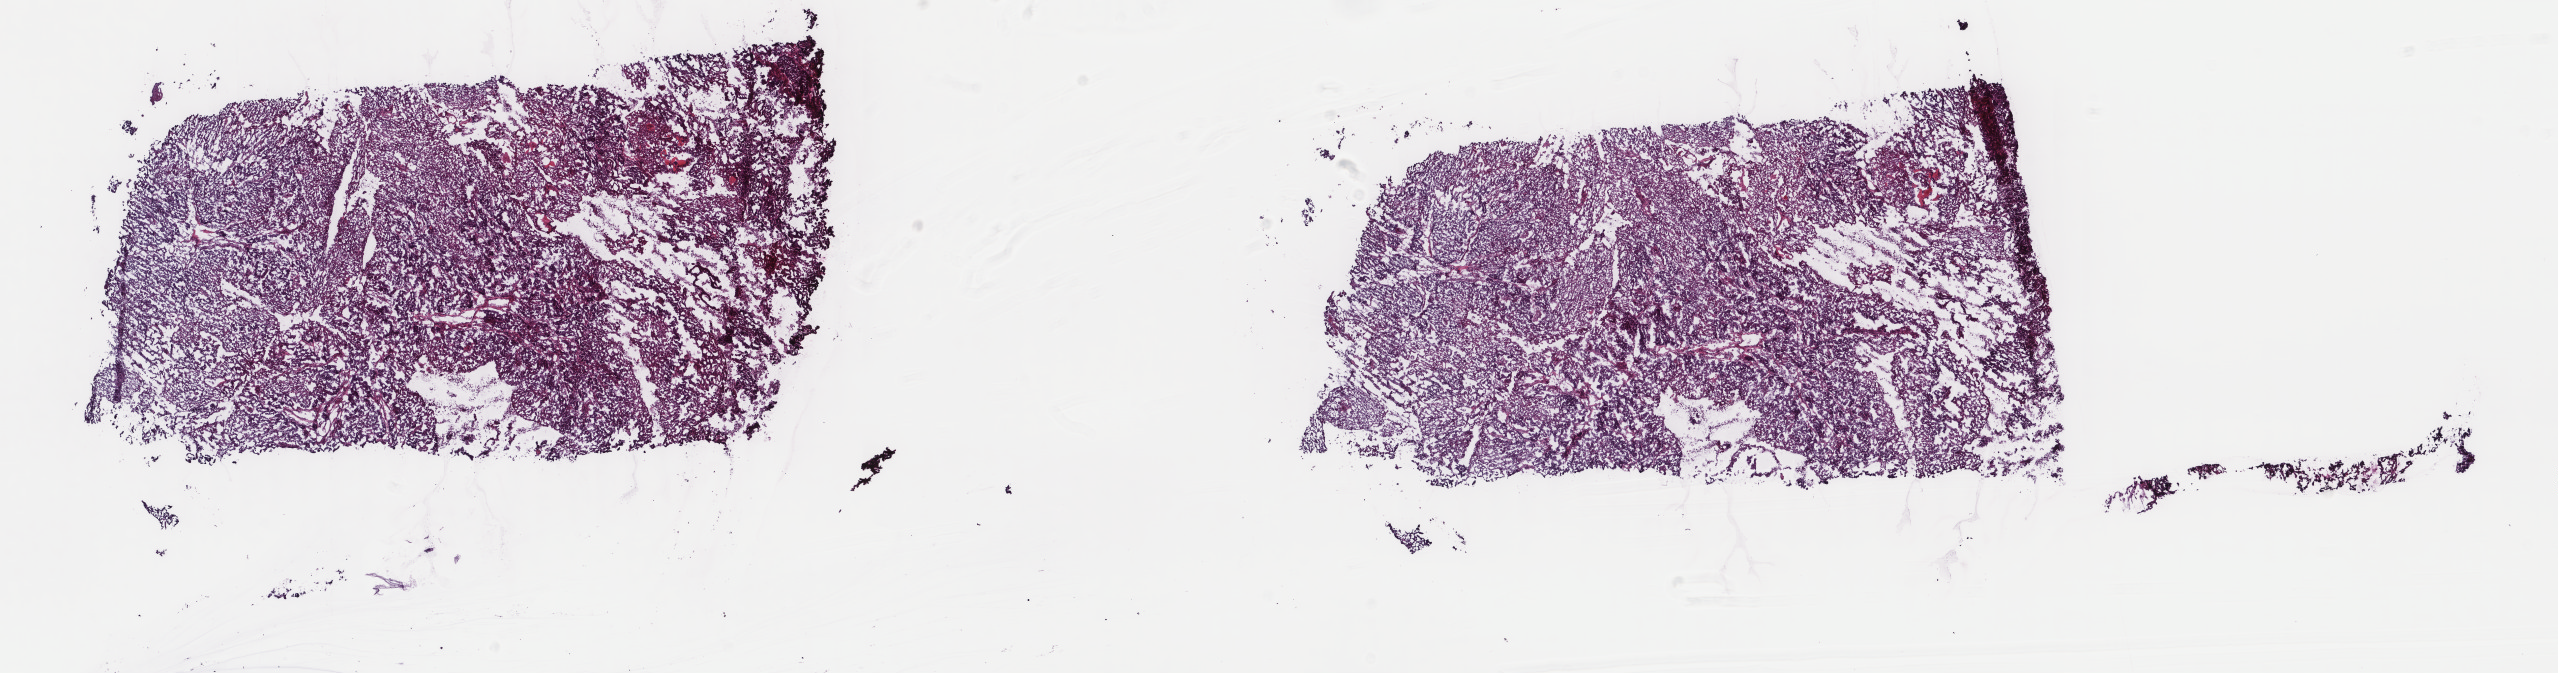
Whole-slide histology image, Hematoxylin and eosin (H&E) stained, shown as a low-resolution overview of the whole scanned area (about 20.3 x 5.3 mm, acquisition: 40x scan); frozen section from the top of the tissue portion; uterus, primary tumour sample. Female patient; age at initial diagnosis 59 years. Histologic grade: G2 (moderately differentiated). Composition of this section per pathologist review: tumour cells 88%, tumour nuclei 90%, normal cells 0%, stromal cells 10%, necrosis 2%. Infiltration values recorded for this section: lymphocyte infiltration 4%, monocyte infiltration 6%, neutrophil infiltration 2%.
• histologic diagnosis: Endometrioid adenocarcinoma, NOS (endometrium)
• lymph nodes positive (case pathology): 2 of 18 examined
• FIGO stage: IIIC1